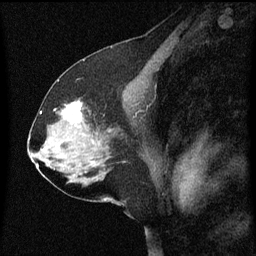
Breast MRI (dynamic contrast-enhanced), one sagittal slice; position 34 of 60 along the scan axis; dynamic contrast-enhanced series, image 2 of 3 at this slice position (ordered by acquisition); 1.5 T; TE 4.2 ms, TR 8 ms; 2 mm slice thickness; 256 × 256 image matrix, field of view 200 × 200 mm. Patient: female, 58 years.
Annotated regions visible in this slice (semi-automatically segmented with operator editing):
- analysis volume of interest (the breast-tissue region the enhancement analysis was run in; not a lesion): bounding box <56,100,95,137> (left, top, right, bottom; pixels)
- tumour enhancement mask (voxels above the 70 % enhancement threshold inside the analysis volume of interest): <62,102,83,123>